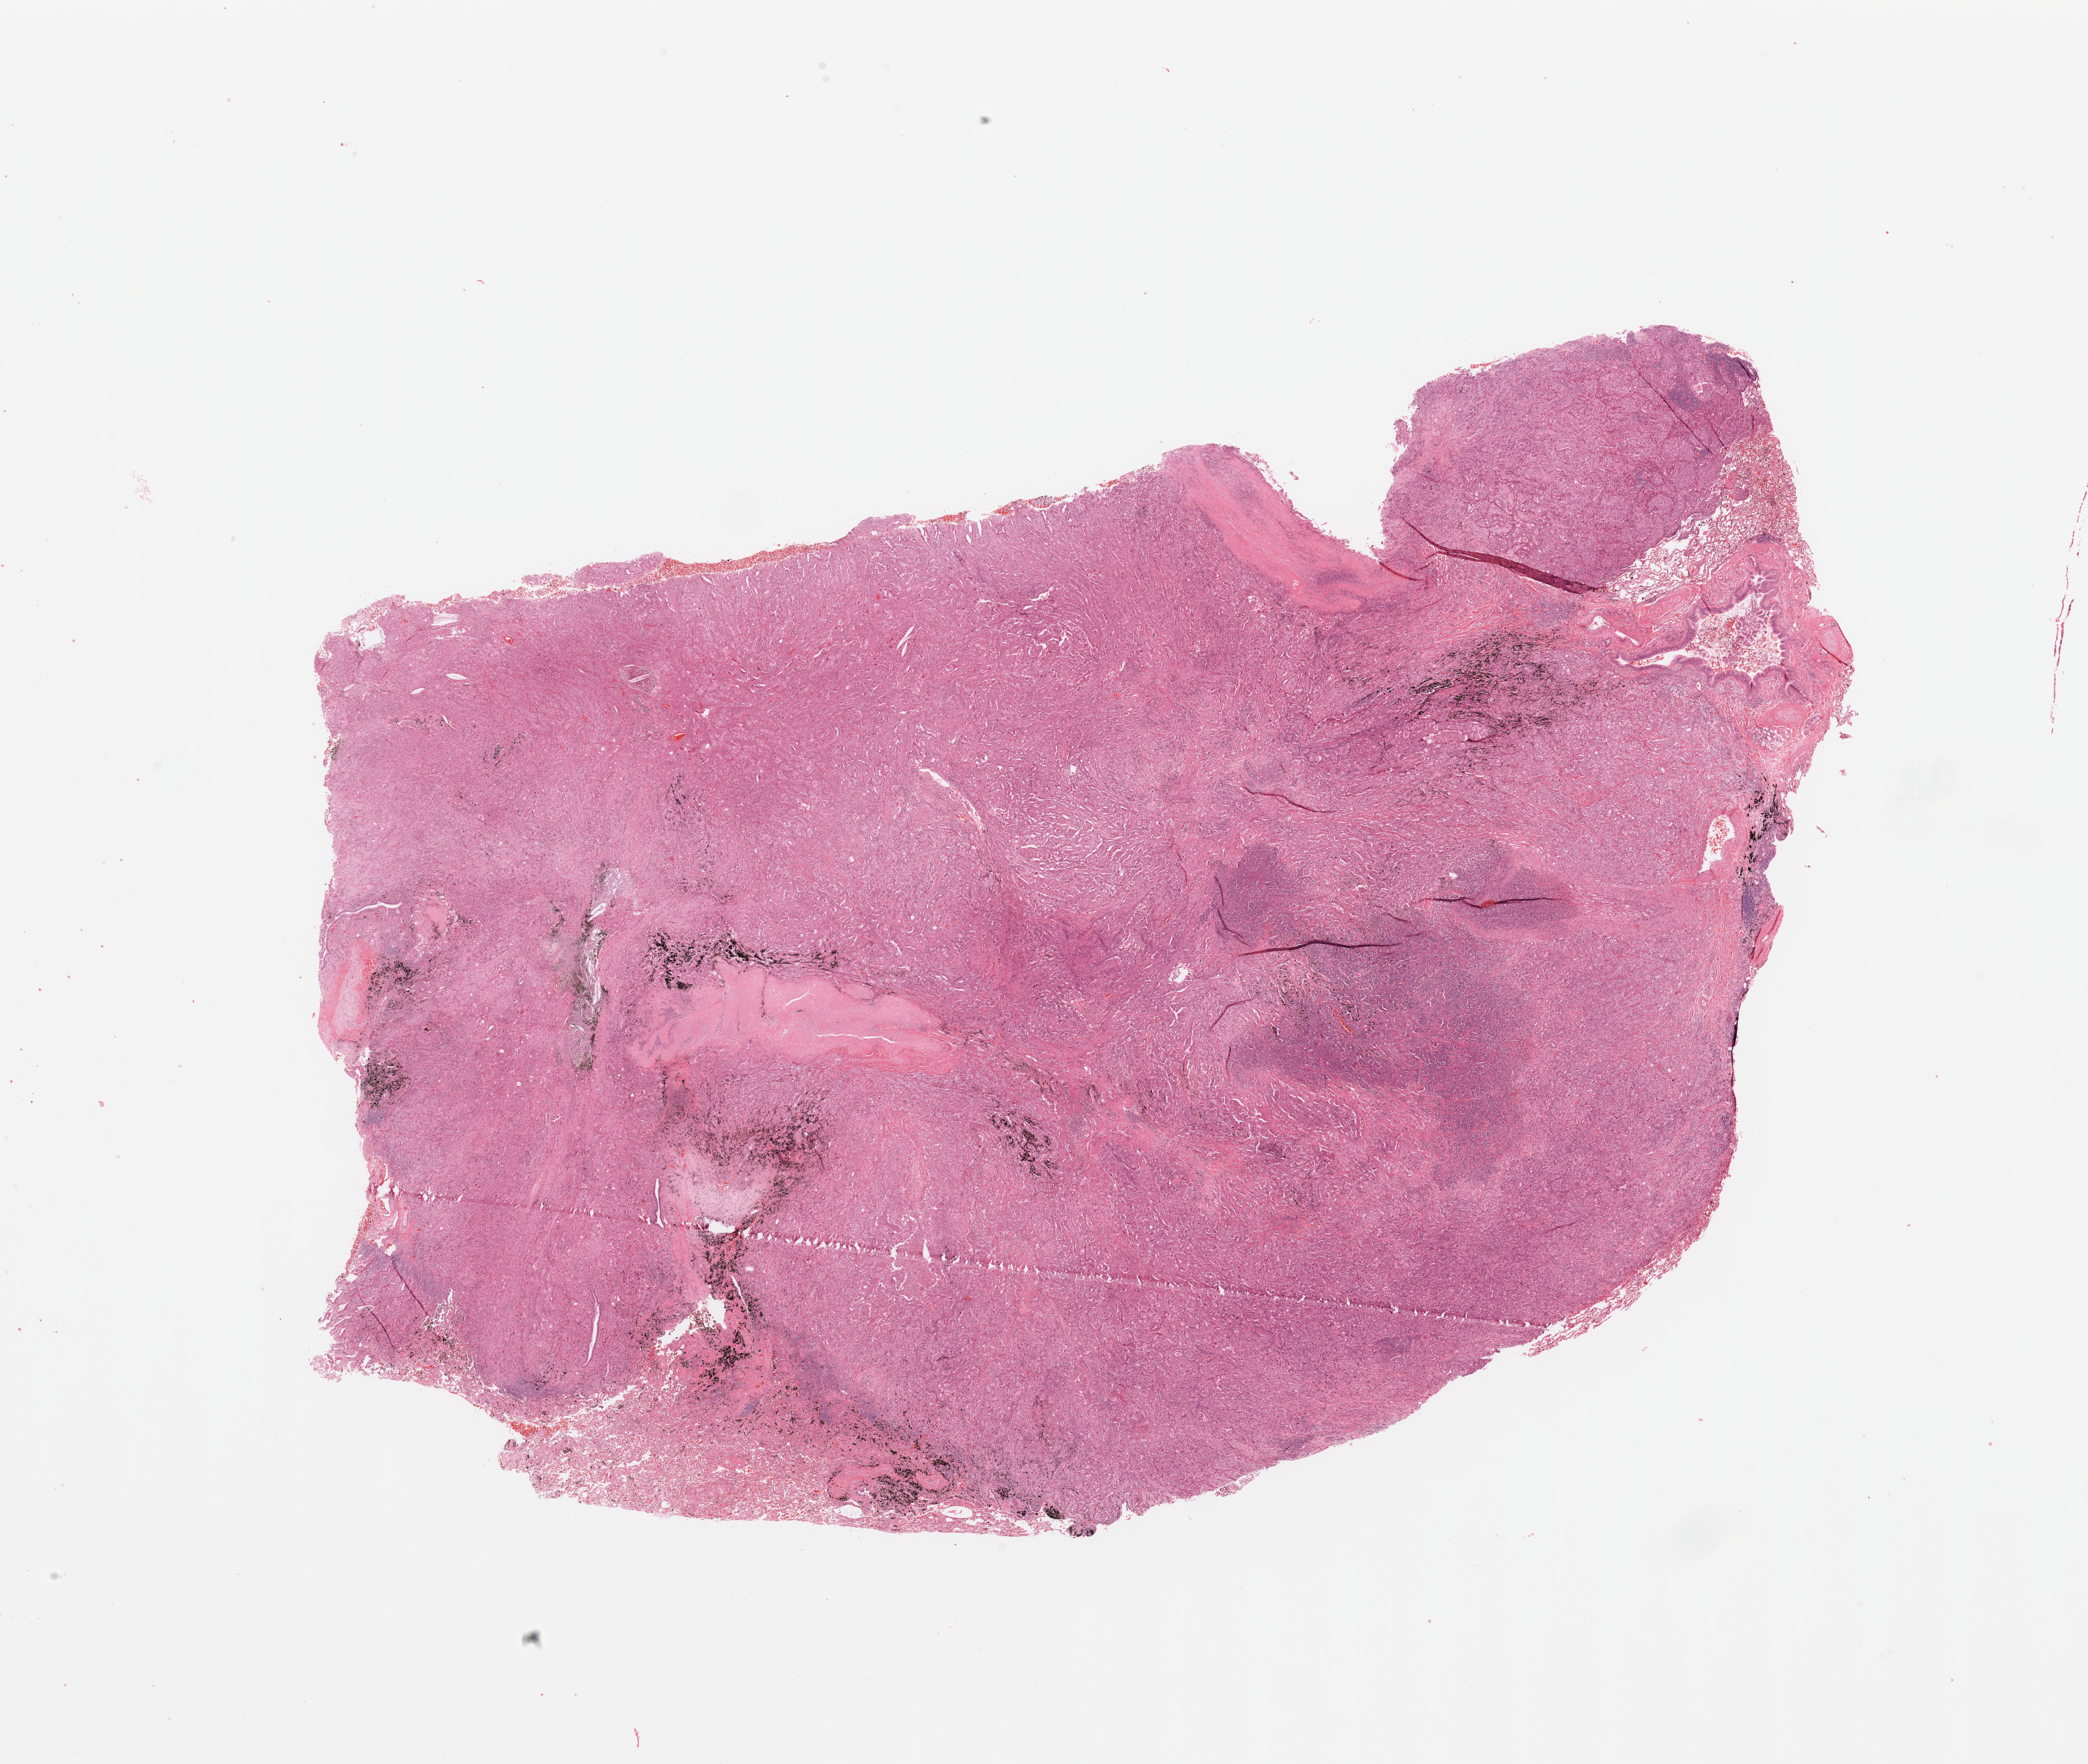
Whole-slide histology image, H&E-stained, whole scanned area (about 23.6 x 20.0 mm, acquisition: 20x scan) shown as a low-resolution overview. Lung, tumour tissue. Patient: male, age 71 years. Histologic grade: G3 (poorly differentiated).
AJCC pathologic stage: IIIA. Histologic diagnosis: Adenocarcinoma, NOS.